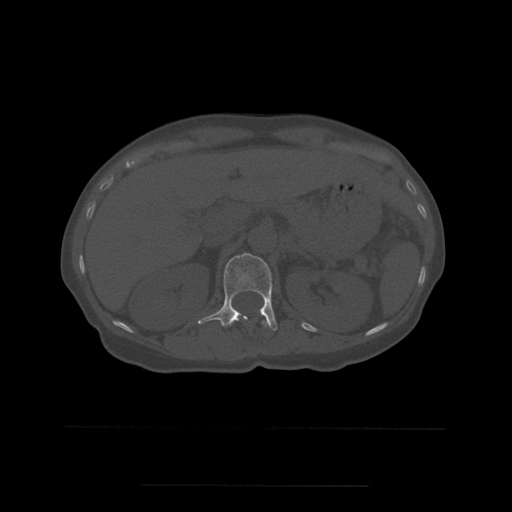
CT including the spine, one axial slice; position 241 of 544 along the scan axis; bone window (W 1800 / L 400 HU); 1.25 mm slice thickness; 512 × 512 image matrix. Patient age 58 years. From the clinical record (not read from this slice): primary cancer: lung.
Outlined on this slice (semi-automatic segmentation, software-assisted and operator-edited):
- L1 vertebra: box from (x=198, y=253) to (x=278, y=331) px
- T12 vertebra: (x=262, y=318)–(x=268, y=327)